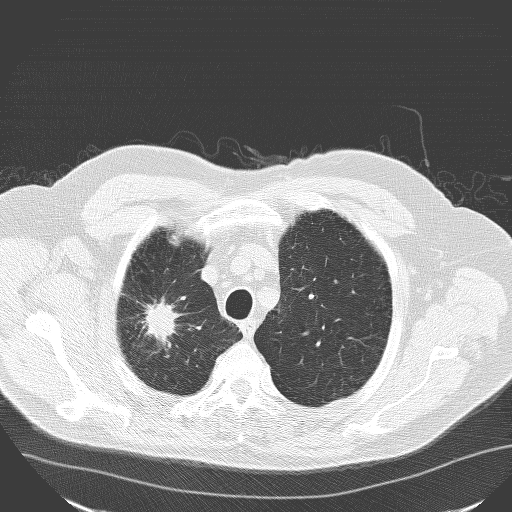
Low-dose screening chest CT, one axial slice; slice 135 of 160 in the series (ordered by position); 120 kVp; lung window (W 1500 / L -600 HU); 3.2 mm slice thickness; 512 × 512 image matrix.
Annotated regions visible in this slice (manually delineated by an expert):
- lesion 1 (tumor, upper lobe of right lung): bounding box <144,301,178,339> (left, top, right, bottom; pixels)